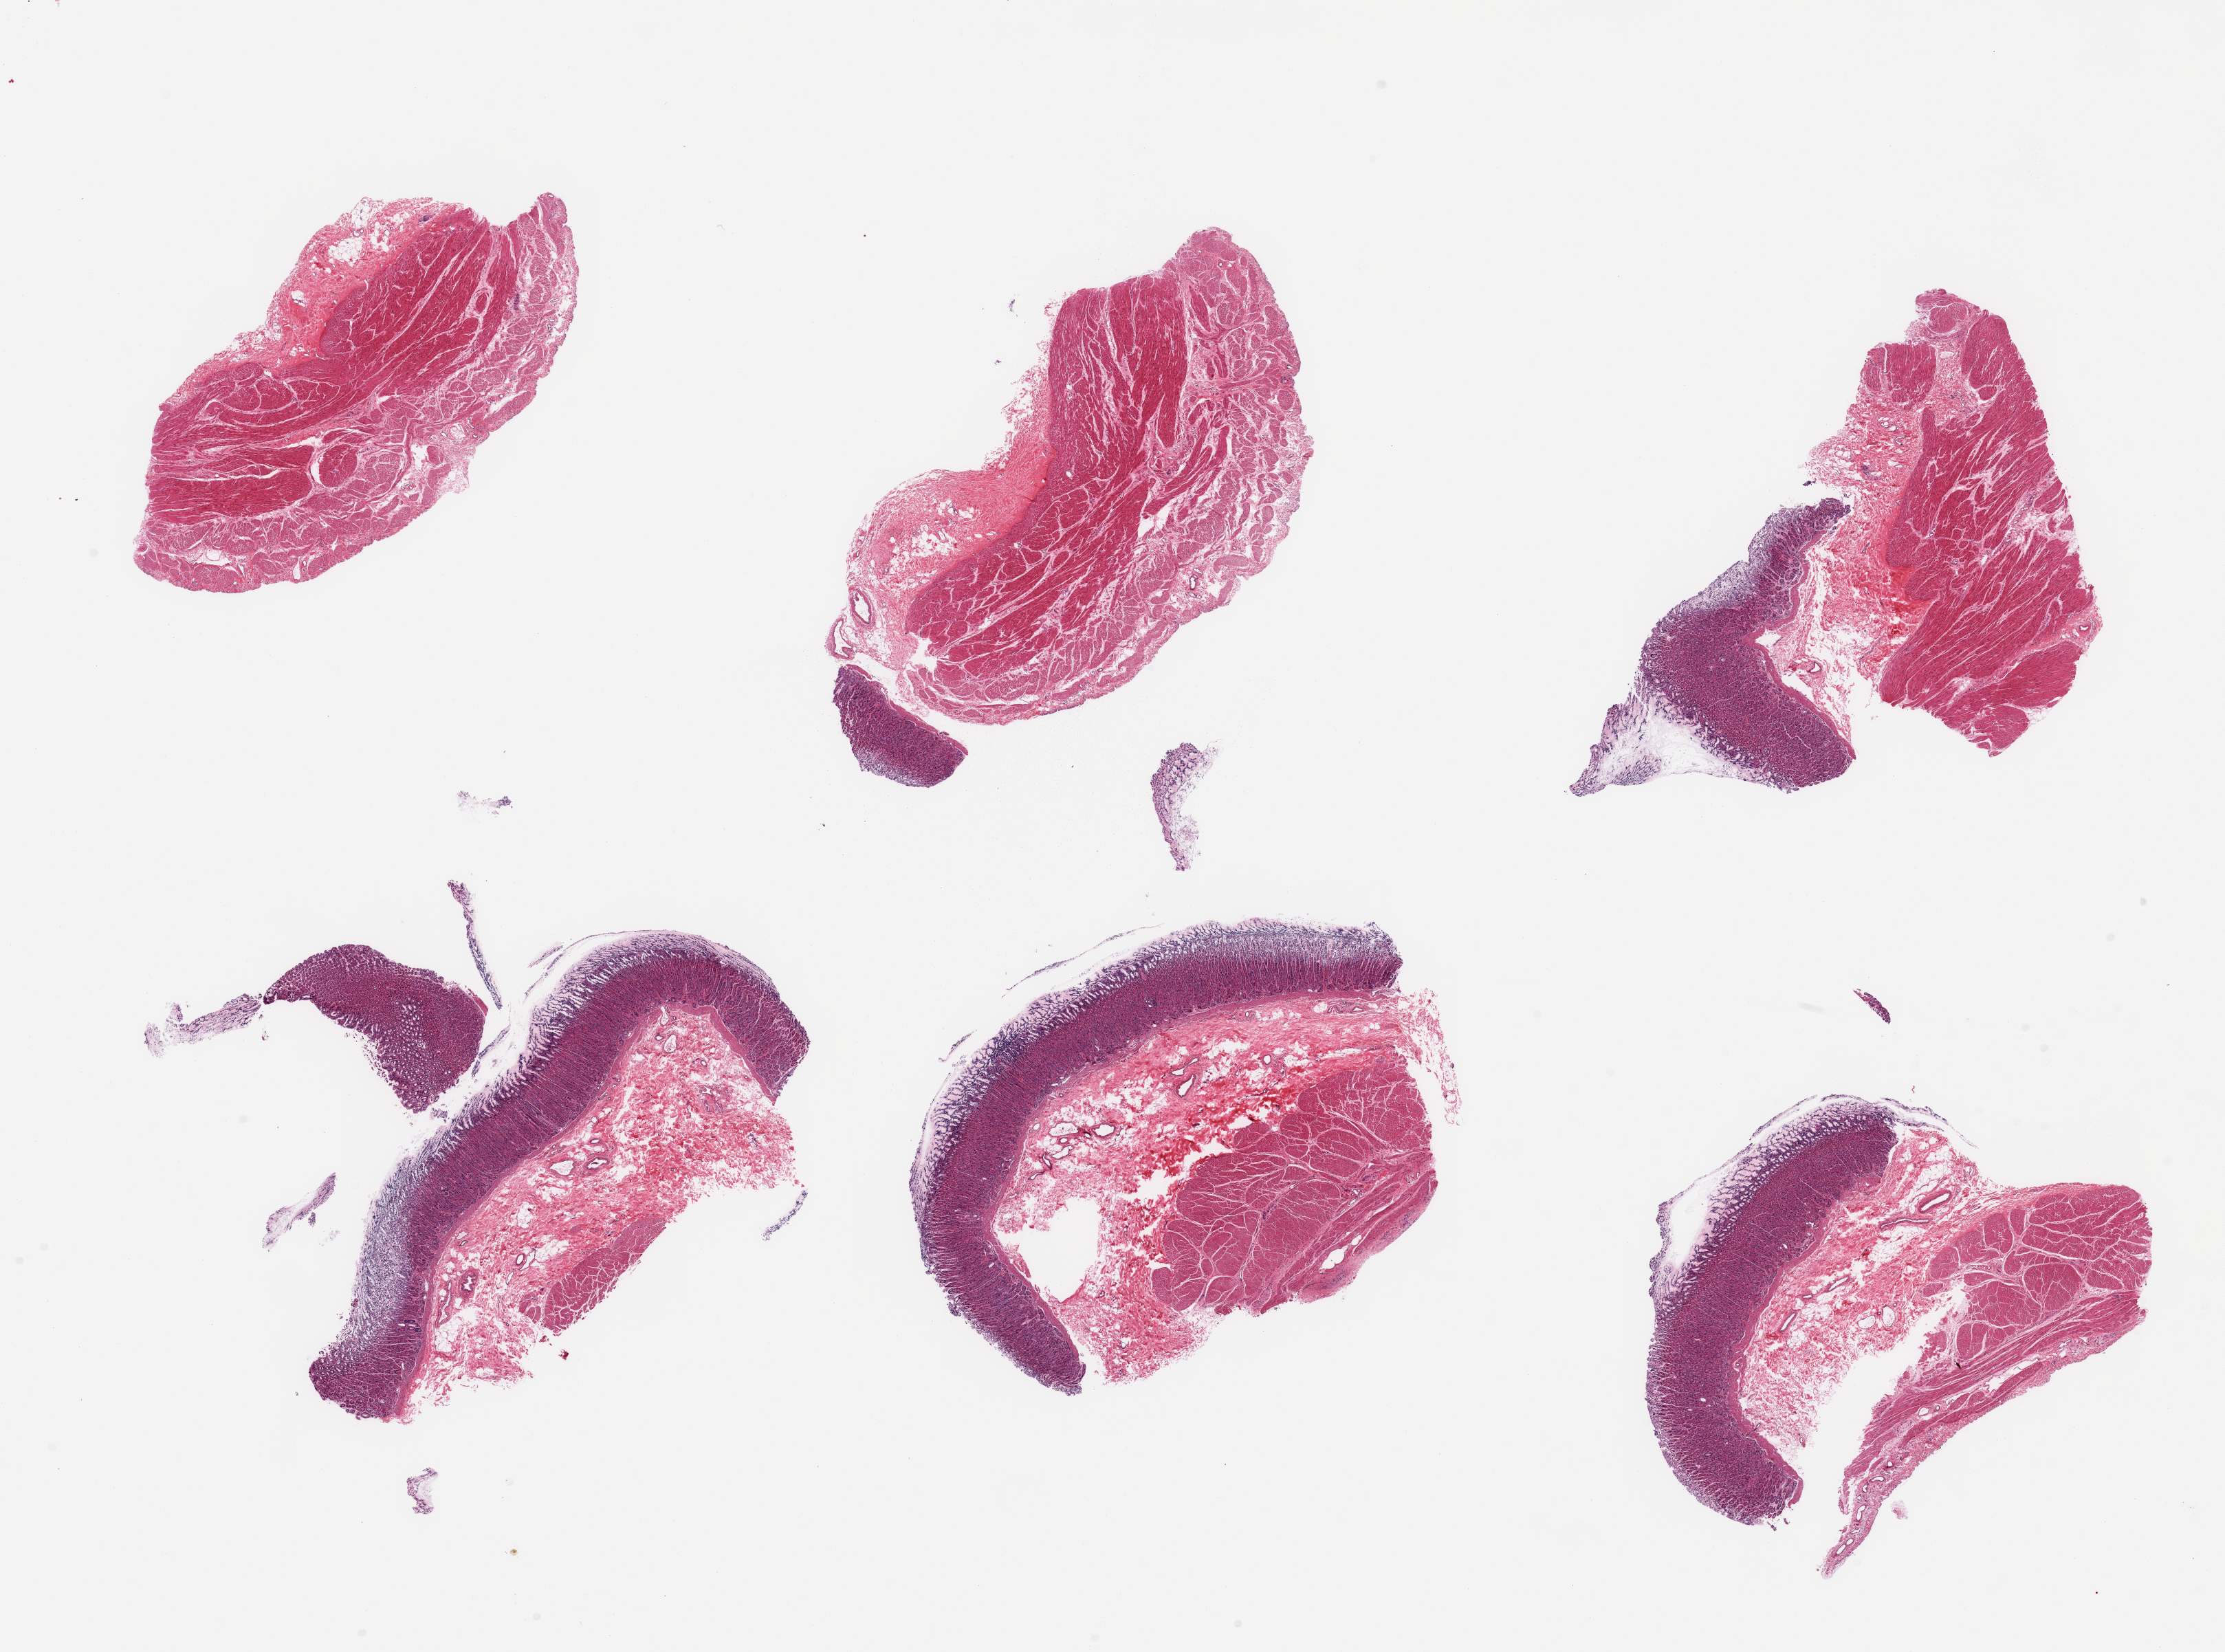
Whole-slide image, haematoxylin and eosin stain, brightfield — whole scanned area (about 25.6 x 19.0 mm) shown as a low-resolution overview, PAXgene-fixed paraffin-embedded (PFPE) section, sampled site (target tissue): stomach, donor tissue sample. Male donor.
Pathologist's review note for this sample: 6 pieces; 5 with mucosa and muscularis; one represents muscularis only.